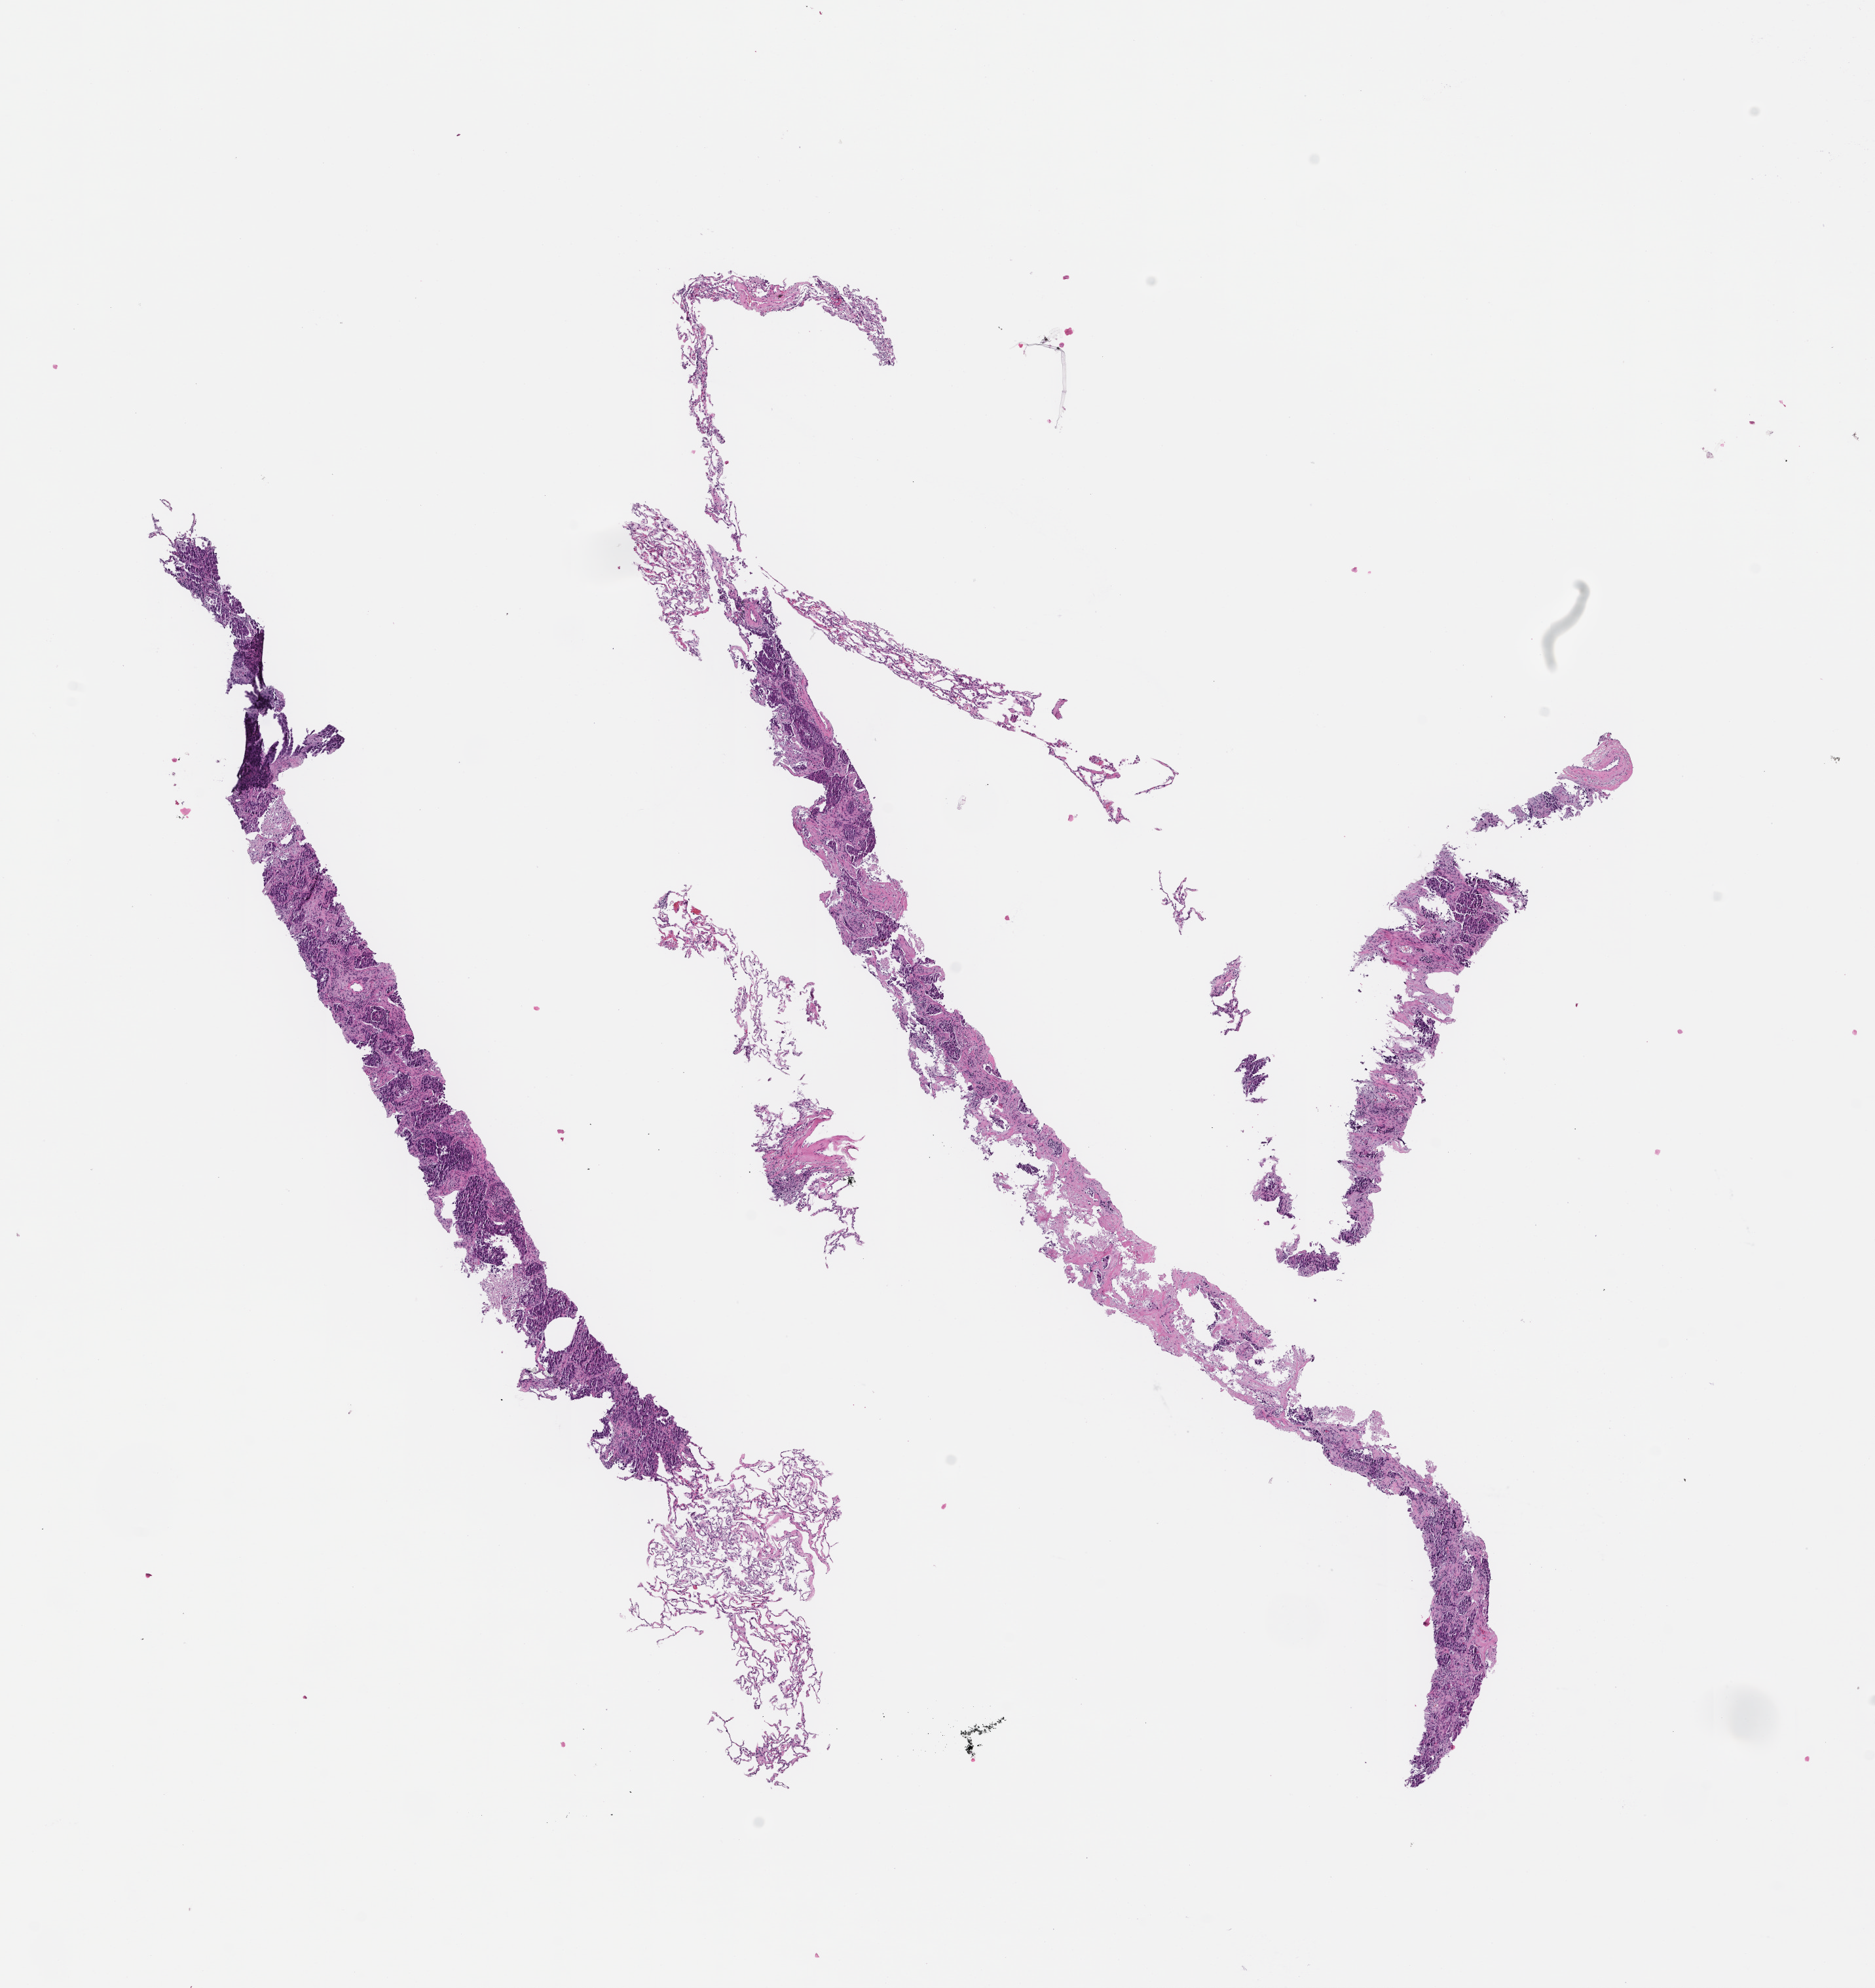
Haematoxylin and eosin whole-slide image, low-resolution overview of the scanned area, about 11.6 x 12.3 mm, formalin-fixed paraffin-embedded section. Patient: female.
* this section: metastasis (sampled organ not recorded)
* primary diagnosis of the patient: Invasive Breast Carcinoma